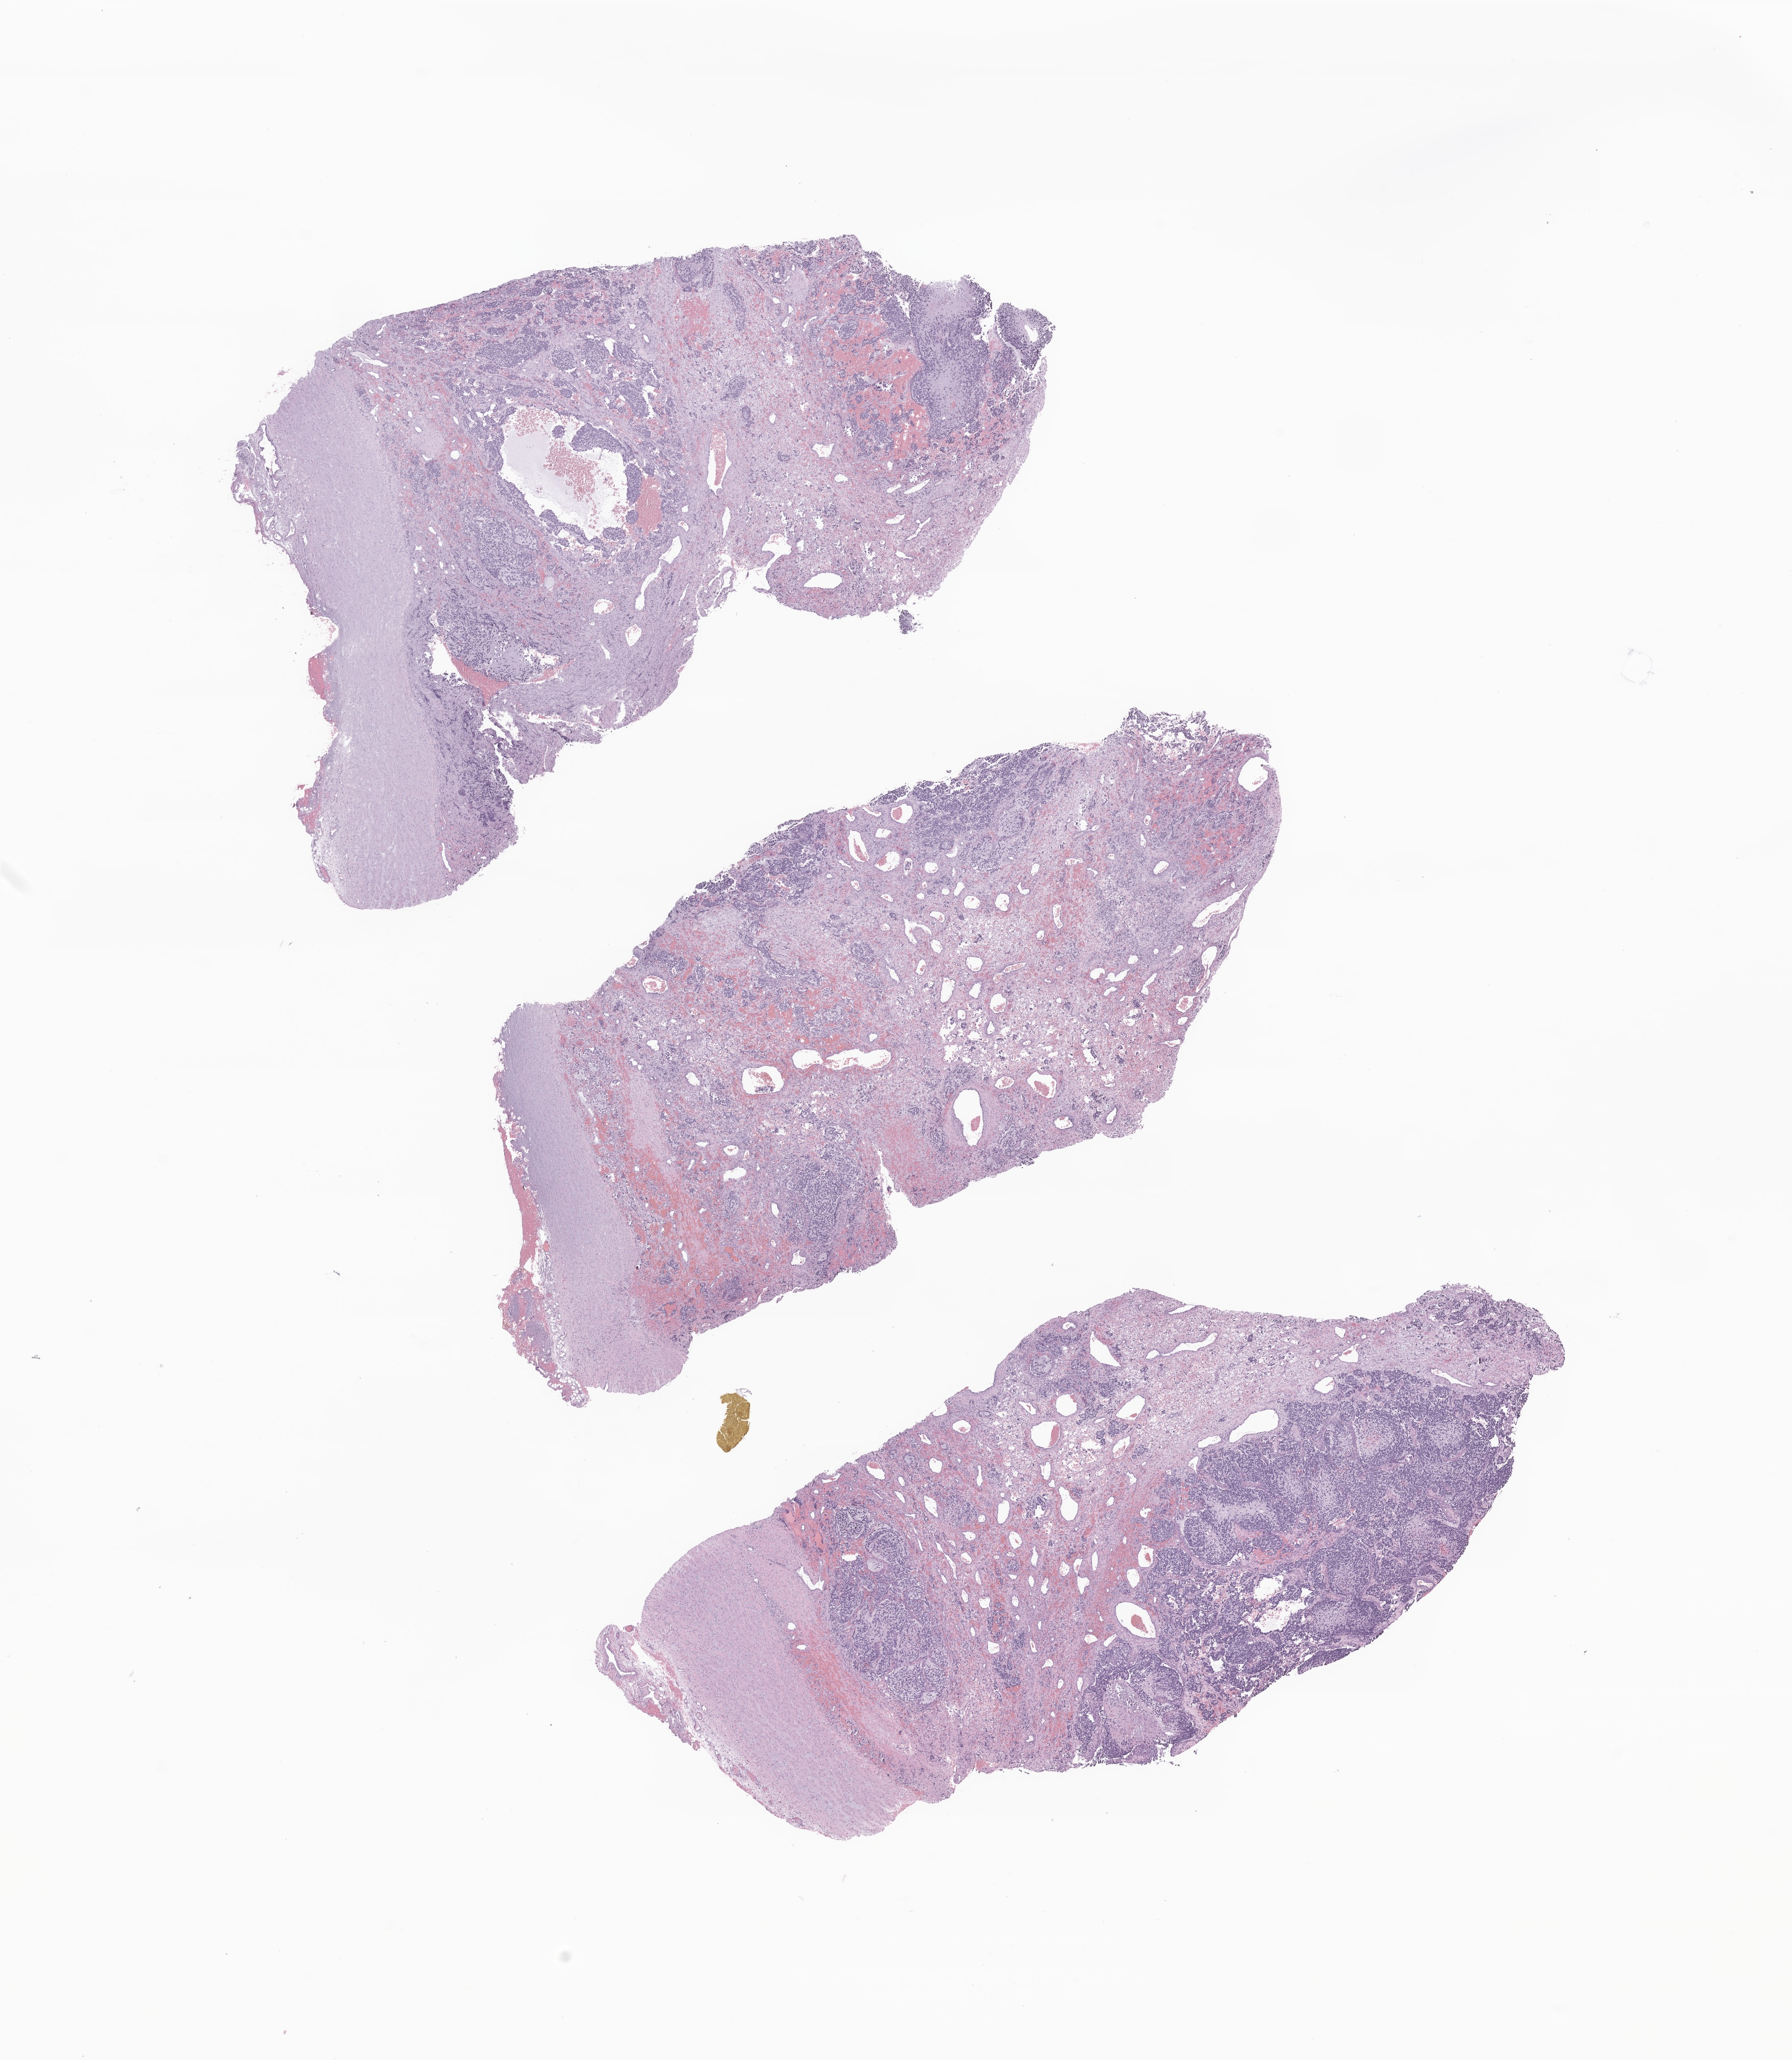
Whole-slide image, H&E stain of tumor tissue from the abdomen — low-resolution overview of the scanned area, about 15.4 x 17.7 mm; formalin-fixed, paraffin-embedded (FFPE) tissue. Male patient, age 240 days.
Recorded diagnosis: Neuroblastoma, NOS.